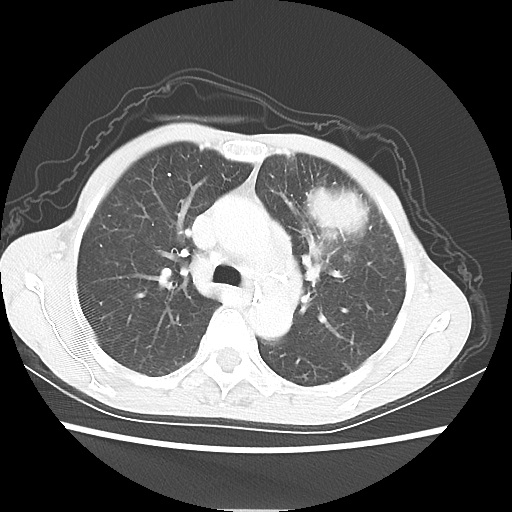
Chest CT, one axial slice; reconstruction kernel LUNG; lung window (W 1500 / L -600 HU); 5 mm slice thickness; 512 × 512 image matrix. Patient: female, 60 years. From the clinical record (not read from this slice): clinical TNM (as recorded): T4 N1 M0.
Structures marked on this image (rectangle marked by the reading radiologist):
- lung tumour (recorded histology: adenocarcinoma): bounding box (x1, y1, x2, y2) in pixels: (295, 177, 384, 249)